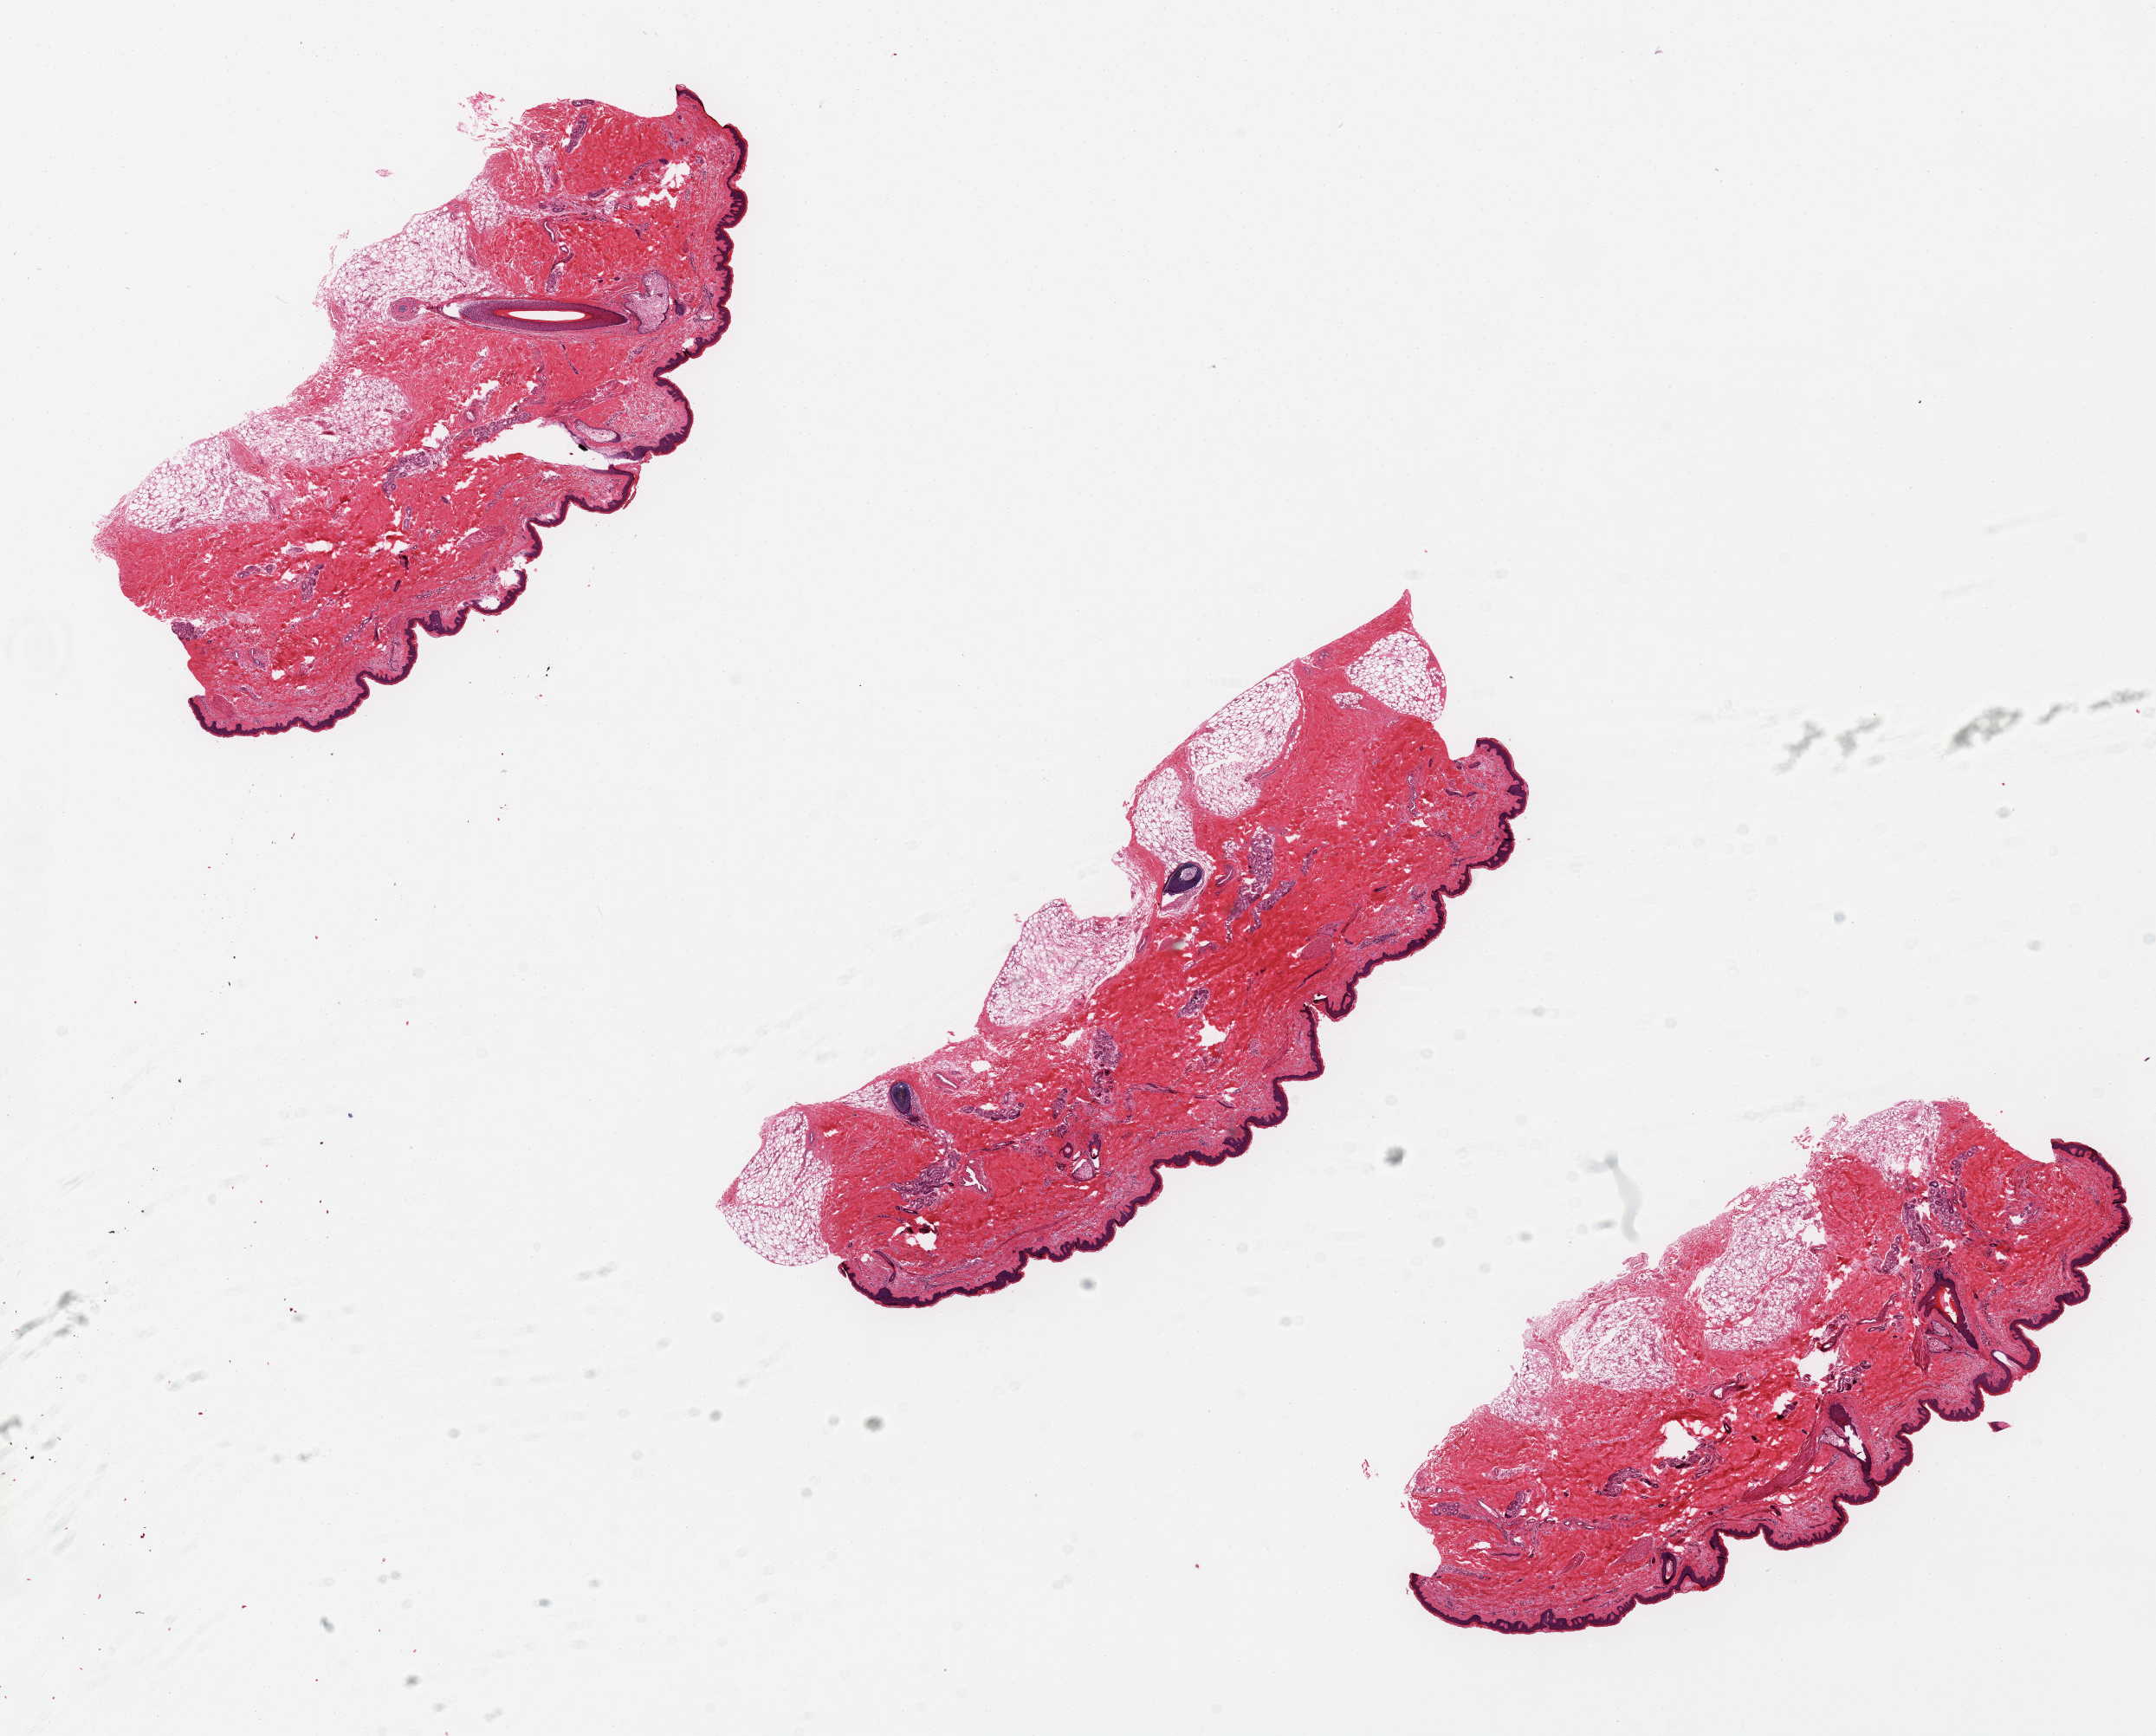
Digitized haematoxylin and eosin-stained section, brightfield — low-resolution overview of the scanned area, about 19.7 x 15.9 mm (slide scanned at 20x); PAXgene-fixed paraffin-embedded (PFPE) section; target tissue: skin of lower leg; tissue donor sample. Male donor.
Review note (as recorded): Epidermis is 2-3% of specimen thickness. Areas of poor fixation, subcutaneous fat.